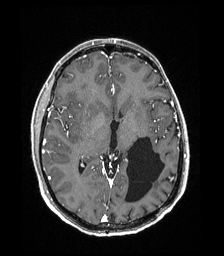
Brain MRI from a brain-tumour surgery series, one axial slice. Position 98 of 192 along the scan axis. T1-weighted post-contrast. 1 mm slice thickness. 224 × 256 image matrix, field of view 224 × 256 mm. From the clinical record (not read from this slice): histopathology: Low grade glioma; IDH mutation: no.
Structures marked on this image (outlined manually by an expert reader):
- previous resection cavity: box from (x=125, y=137) to (x=164, y=203) px